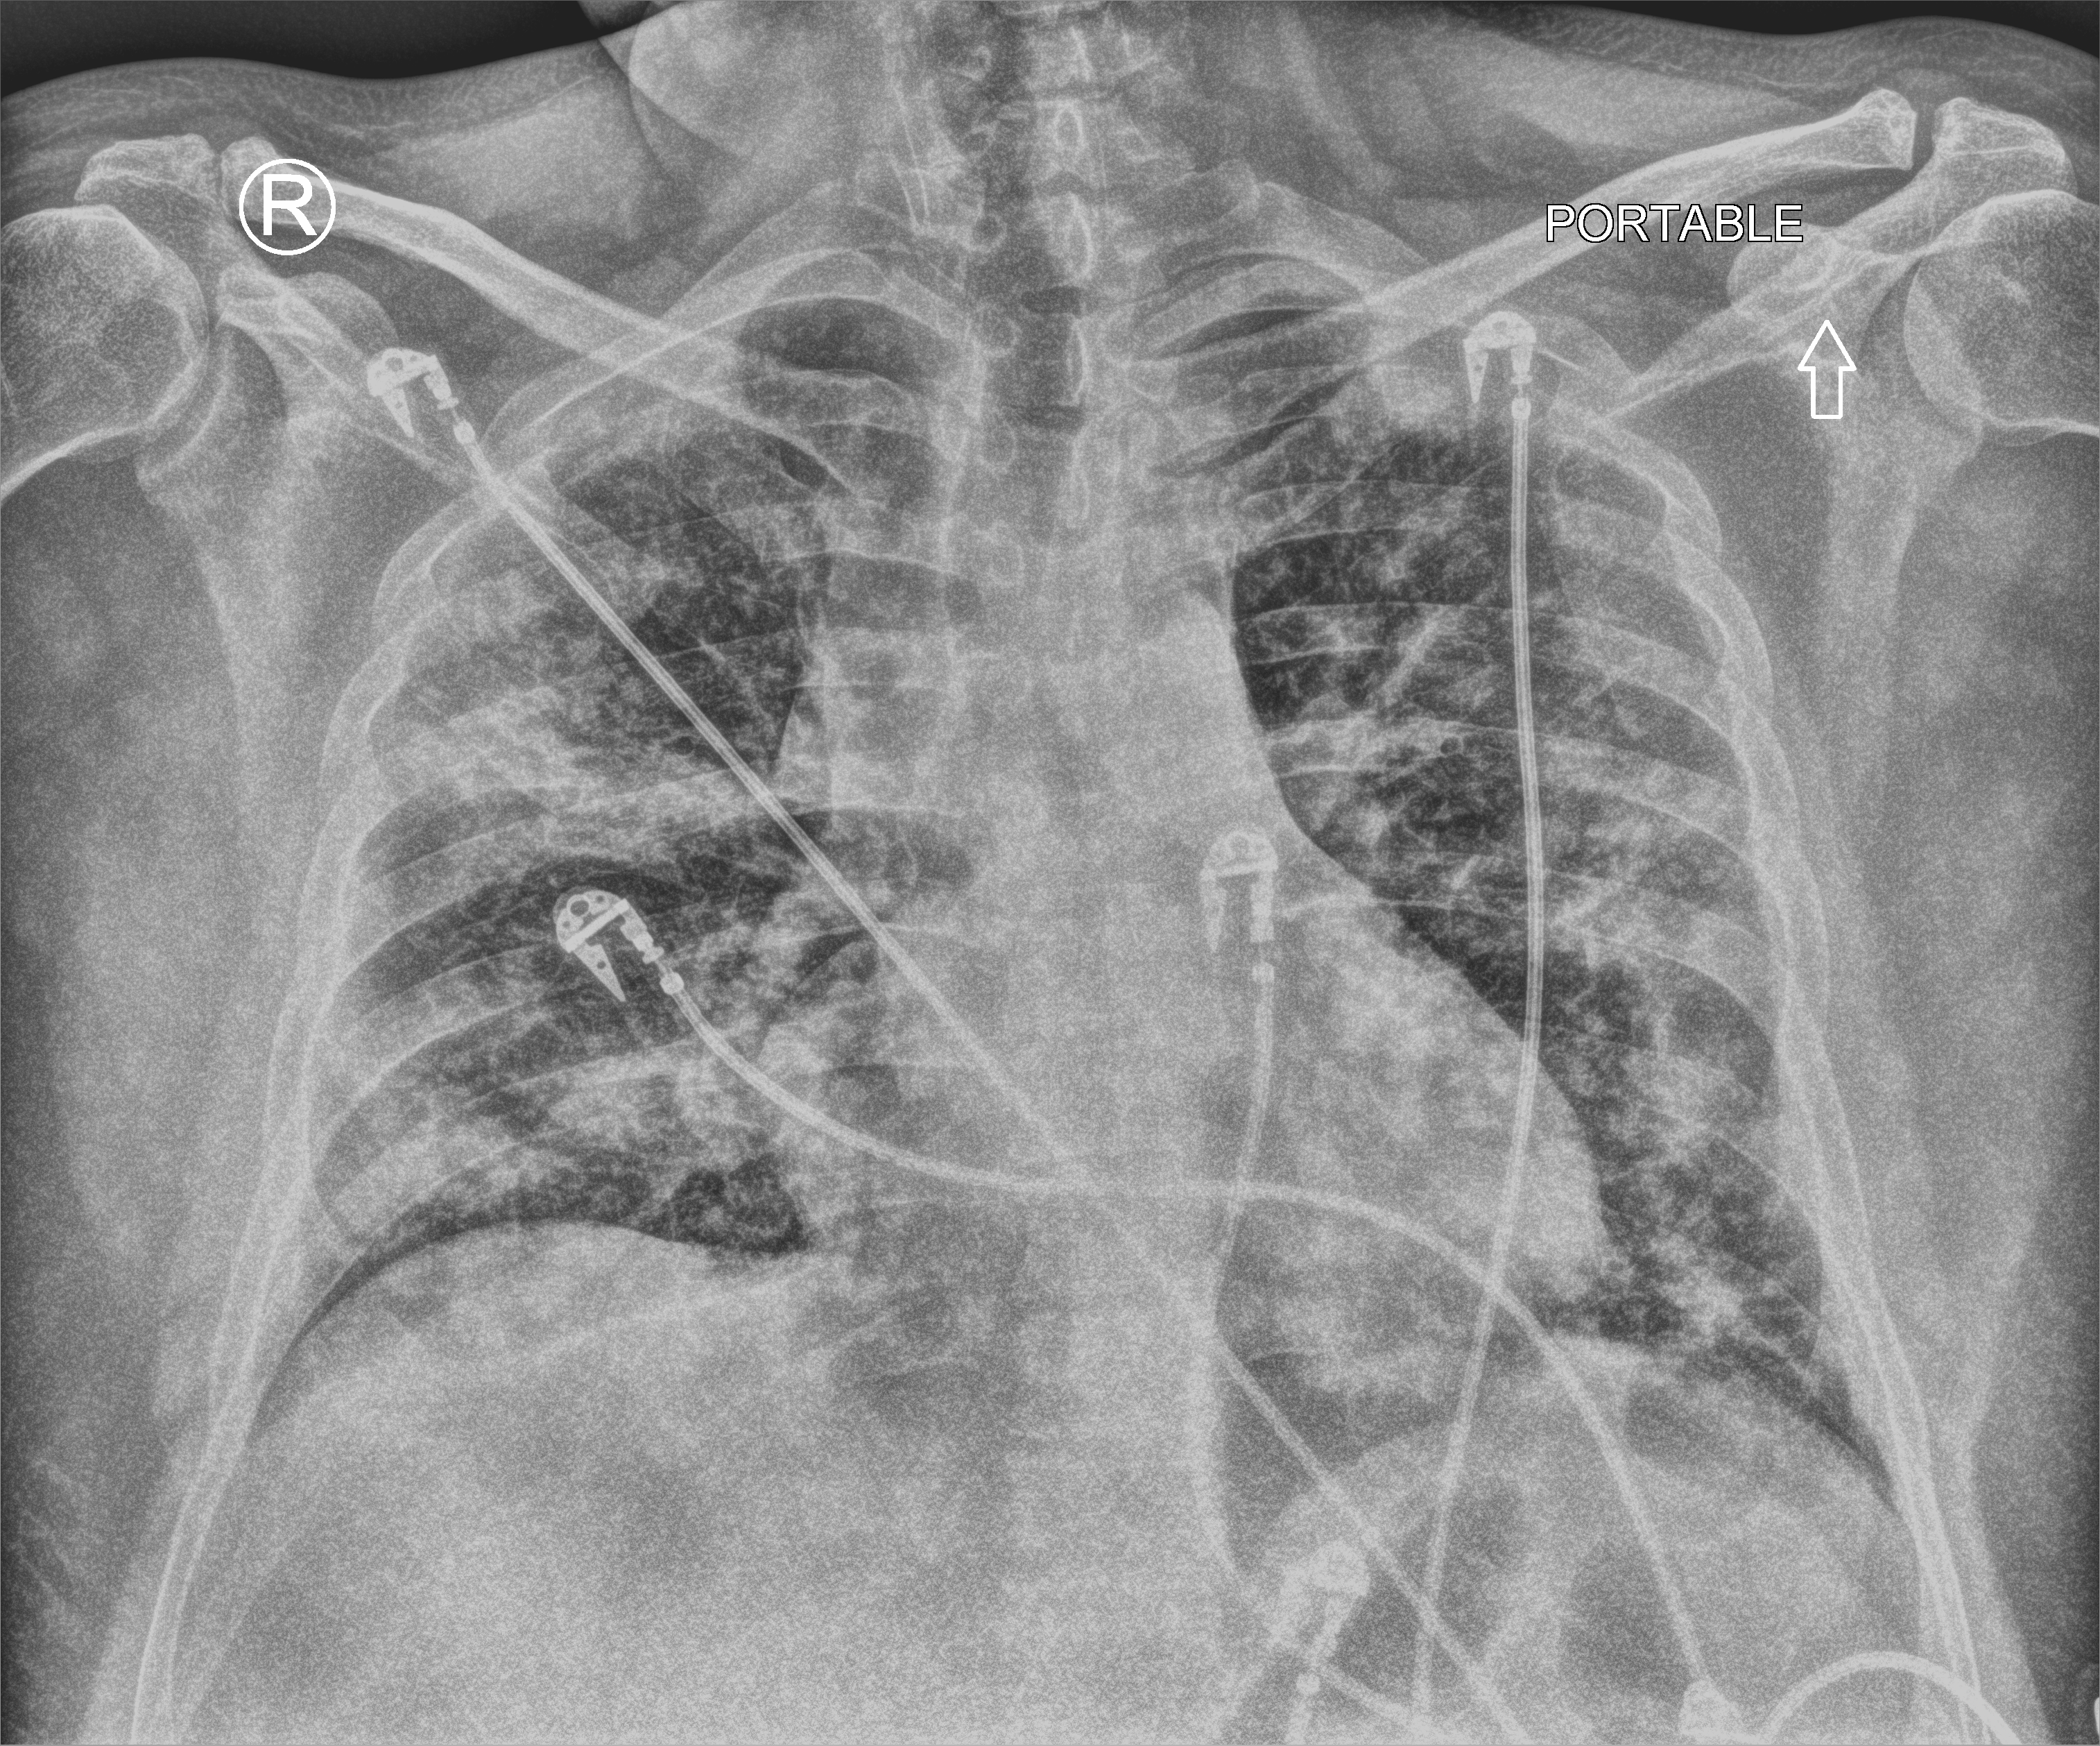
Bedside chest radiograph (computed radiography), anteroposterior (AP) projection. Adult patient hospitalised with COVID-19, age 18–59 years.
Hospital-stay facts (about this admission, not read from this image; timing relative to this image not recorded):
- admitted to intensive care during this hospital stay: yes